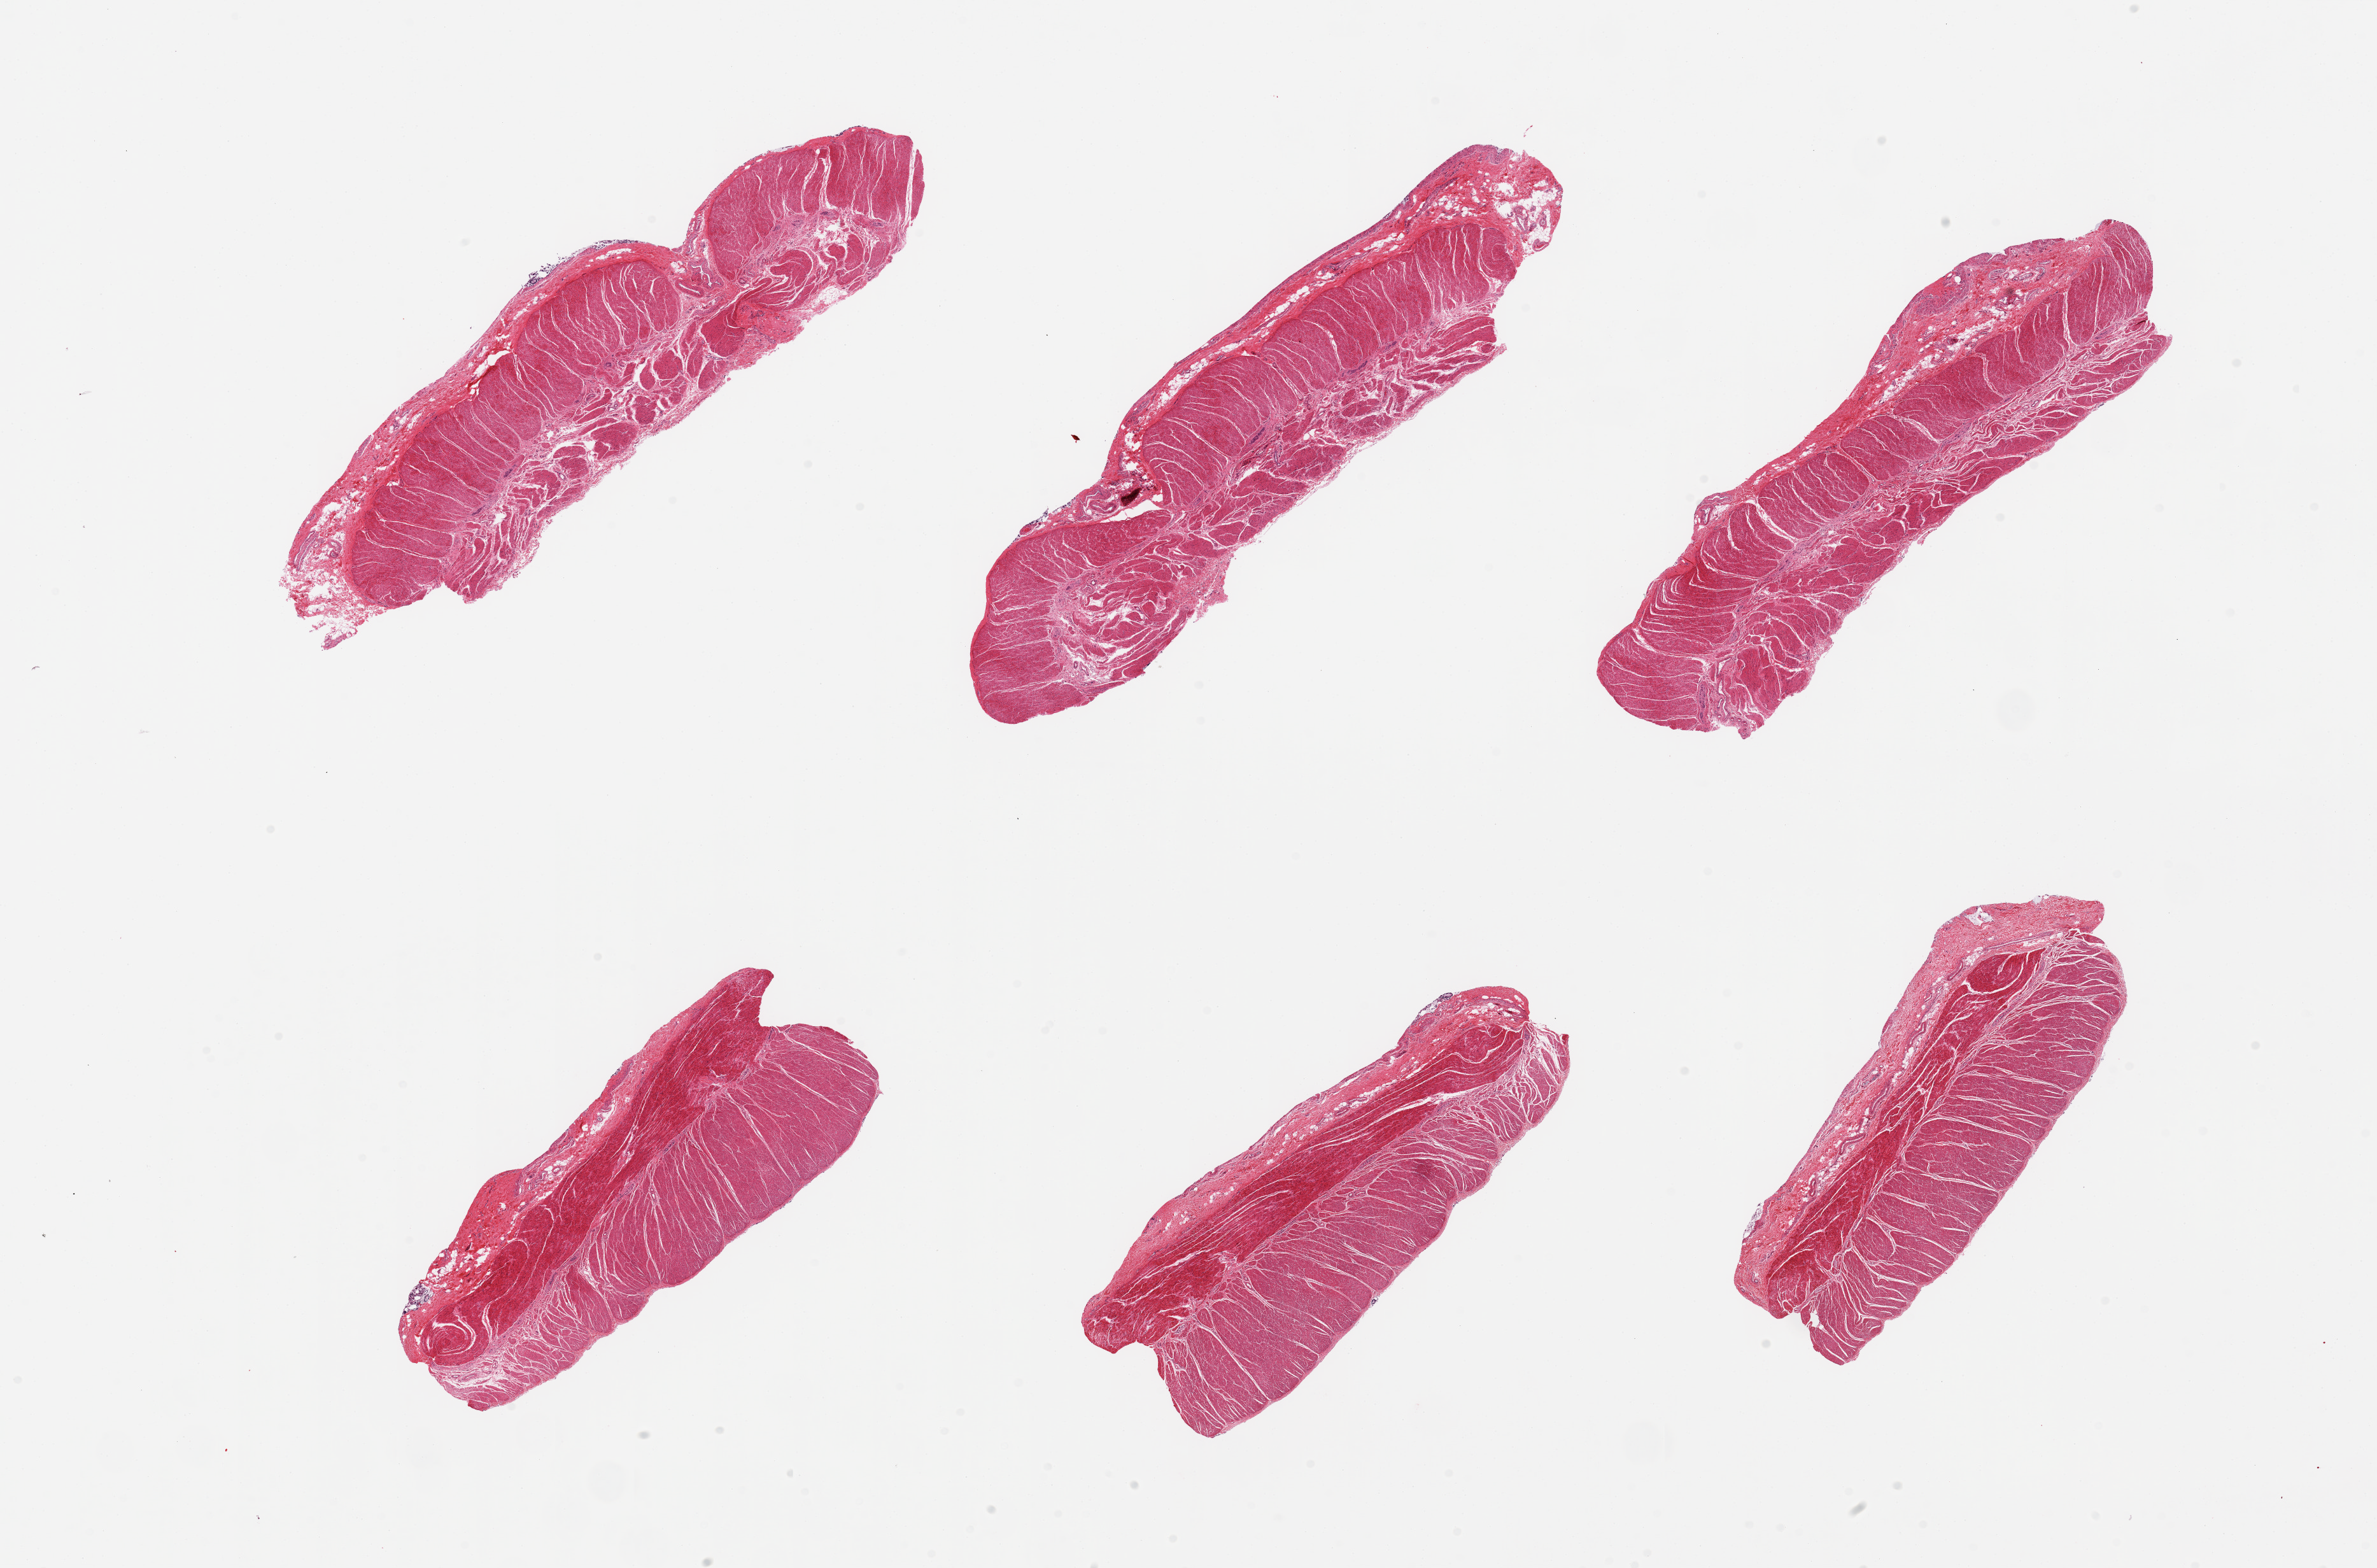
Digitized hematoxylin and eosin (H&E)-stained section, whole scanned area (about 29.5 x 19.5 mm, acquisition: 20x scan) shown as a low-resolution overview, PAXgene-fixed, paraffin-embedded tissue, sampled site (target tissue): sigmoid colon, tissue donor sample. Donor sex: male.
Pathologist's review note for this sample: 6 pieces, all muscularis.